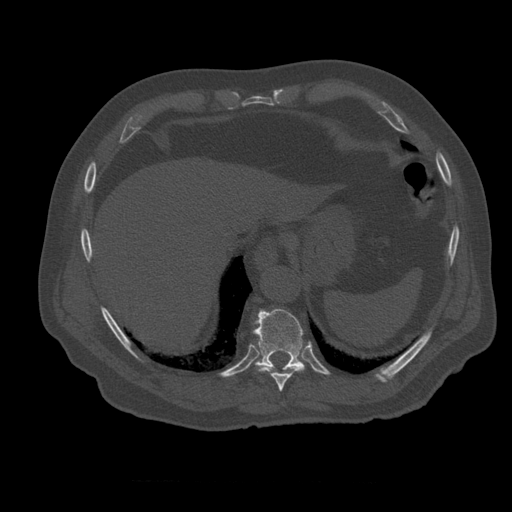
CT including the spine, one axial slice; position 309 of 399 along the scan axis; reconstruction kernel STANDARD; 120 kVp; bone window (W 1800 / L 400 HU); 1.25 mm slice thickness; 512 × 512 image matrix. Patient age 73 years. From the clinical record (not read from this slice): primary cancer: prostate; vertebrae with lytic lesions (as recorded): L2.
Annotated regions visible in this slice (semi-automatically segmented with operator editing):
- T10 vertebra: bounding box [x1, y1, x2, y2] px = [254, 309, 318, 372]
- T12 vertebra: [267, 347, 280, 359]
- T9 vertebra: [256, 363, 305, 392]